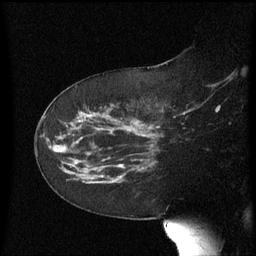
Breast MRI (dynamic contrast-enhanced), one sagittal slice. Slice 35 of 60 in the series (ordered by position). Dynamic contrast-enhanced series, image 2 of 3 at this slice position (ordered by acquisition). 1.5 T. TE 4.2 ms, TR 8.4 ms. 256 × 256 image matrix, field of view 200 × 200 mm. Female patient, age 63 years. Case-level facts recorded for this patient, not image findings: setting: breast cancer imaged before/during neoadjuvant chemotherapy; receptor status: HER2-positive.
Outlined on this slice (semi-automatic segmentation, software-assisted and operator-edited):
- analysis volume of interest (the breast-tissue region the enhancement analysis was run in; not a lesion): bounding box <66,136,138,185> (left, top, right, bottom; pixels)
- tumour enhancement mask (voxels above the 70 % enhancement threshold inside the analysis volume of interest): <119,166,124,167>